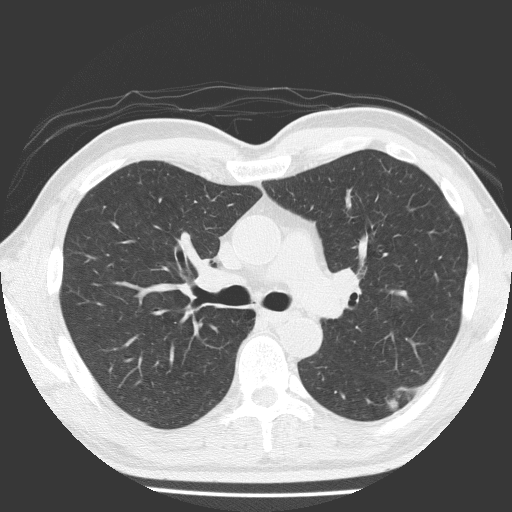
Chest CT (low-dose screening protocol), one axial image. Baseline screening round. Lung window (W 1500 / L -600 HU). 2 mm slice thickness. 120 kVp. Slice 70 of 184 in the series. Male, age 58 years at enrolment. Current smoker at enrolment.
Lesion marked by an expert reader, bounding box (x1, y1, x2, y2) in pixels: (374, 373, 424, 423). The screening reader recorded 4 non-calcified nodules or masses ≥4 mm on this exam (left lower lobe, left lower lobe, right middle lobe, left upper lobe); which of them this box marks is not recorded. Lung cancer was diagnosed 99 days after this screen: adenosquamous carcinoma, left lower lobe, moderately differentiated (G2), stage IA (AJCC 6th edition), 28 mm at pathology.